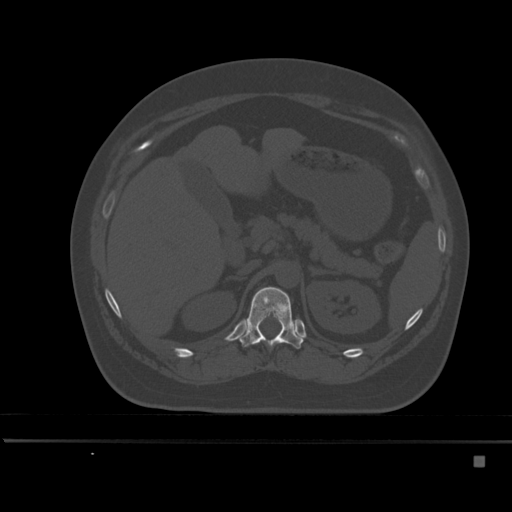
CT including the spine, one axial slice; position 215 of 495 along the scan axis; bone window (W 1800 / L 400 HU); 1.5 mm slice thickness; 512 × 512 image matrix, field of view 404 × 404 mm. Patient: female, 33 years. From the clinical record (not read from this slice): primary cancer: breast; vertebrae with lytic lesions (as recorded): T1.
Structures marked on this image (semi-automatically segmented with operator editing):
- T12 vertebra: bounding box [x1, y1, x2, y2] px = [238, 287, 303, 349]